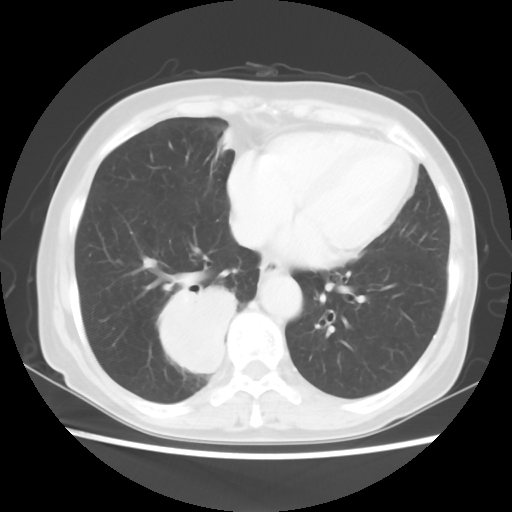
Chest CT, one axial slice. Position 19 of 56 along the scan axis. Lung window (W 1500 / L -600 HU). 512 × 512 image matrix, field of view 332 × 332 mm. Patient: female, 66 years. Case-level facts recorded for this patient, not image findings: clinical TNM (as recorded): T2 N3 M0; histopathological grade: G3.
Structures marked on this image (rectangle marked by the reading radiologist):
- lung tumour (recorded histology: small cell carcinoma): bounding box <163,281,250,393> (left, top, right, bottom; pixels)